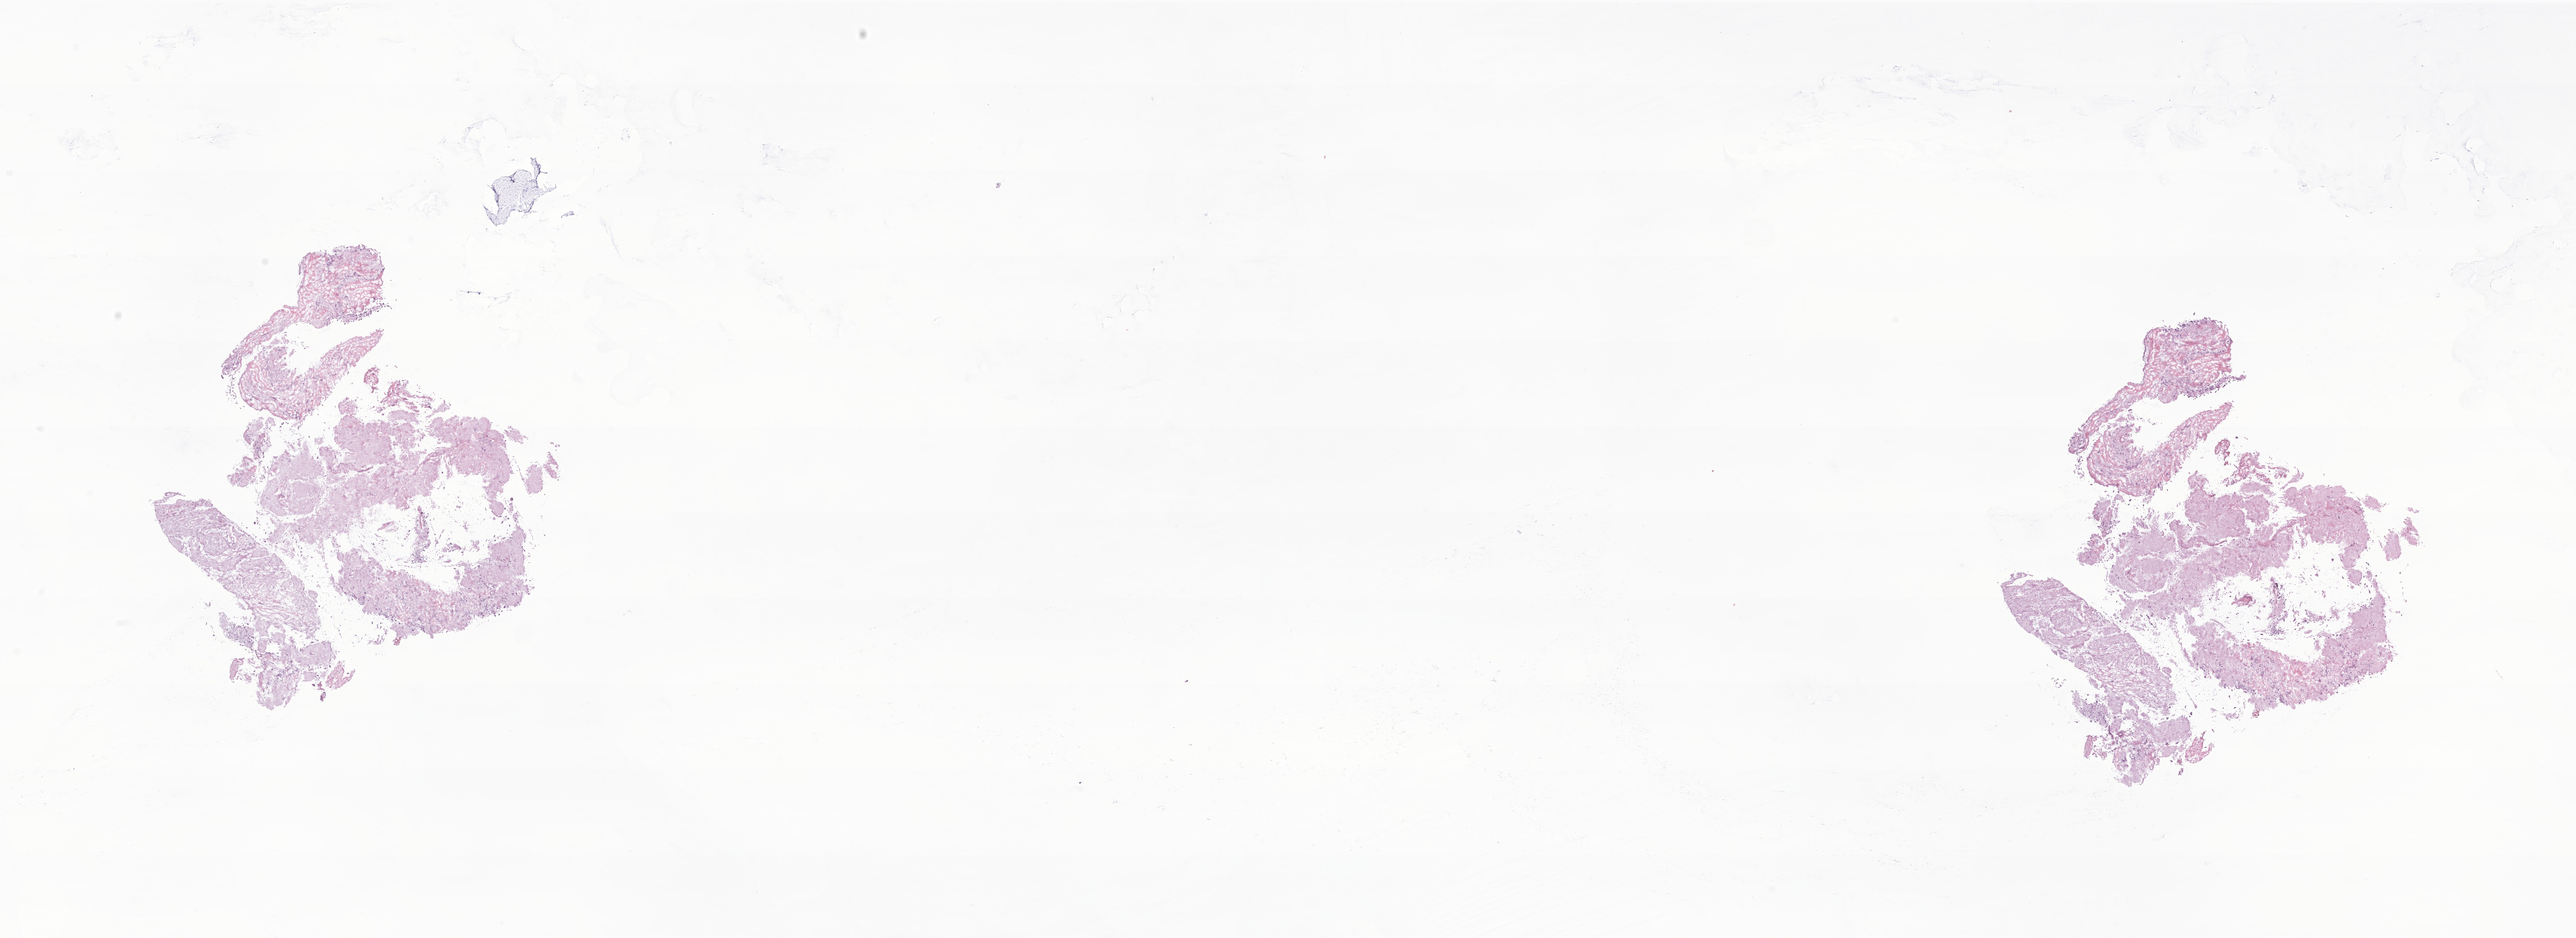
Haematoxylin and eosin whole-slide image of tumor tissue from the posterior mediastinum — whole scanned area (about 32.1 x 11.7 mm) shown as a low-resolution overview; frozen section. Patient female; age 40 months (3 years 4 months).
• diagnosis: Neuroblastoma, NOS